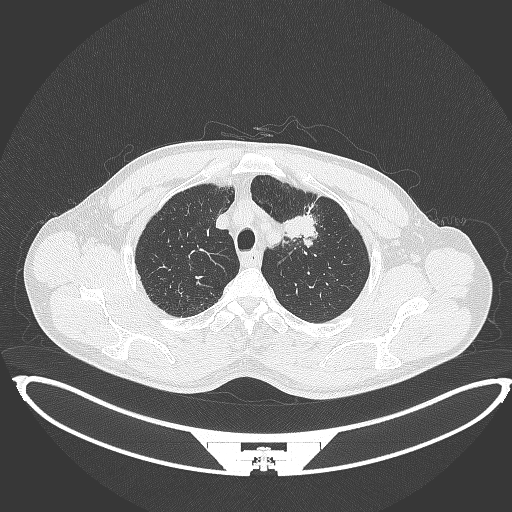
Chest CT, one axial slice; slice 364 of 395 in the series (ordered by position); reconstruction kernel B70f; 120 kVp; lung window (W 1500 / L -600 HU); 512 × 512 image matrix, field of view 457 × 457 mm. Patient: male, 60 years. Case-level facts recorded for this patient, not image findings: clinical TNM (as recorded): T2a N0 M0; histopathological grade: G1-G2.
Outlined on this slice (bounding box drawn by a radiologist):
- lung tumour (recorded histology: squamous cell carcinoma): bounding box <280,211,320,242> (left, top, right, bottom; pixels)